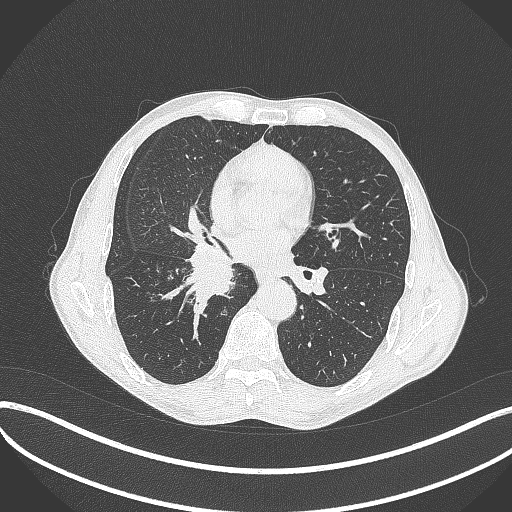
Chest CT, one axial slice; position 213 of 481 along the scan axis; 120 kVp; lung window (W 1500 / L -600 HU); 1 mm slice thickness; 512 × 512 image matrix, field of view 400 × 400 mm. Male patient, age 65 years. From the clinical record (not read from this slice): clinical TNM (as recorded): T2a N0 M0; histopathological grade: G2.
Outlined on this slice (rectangle marked by the reading radiologist):
- lung tumour (recorded histology: squamous cell carcinoma): box from (x=178, y=243) to (x=237, y=311) px